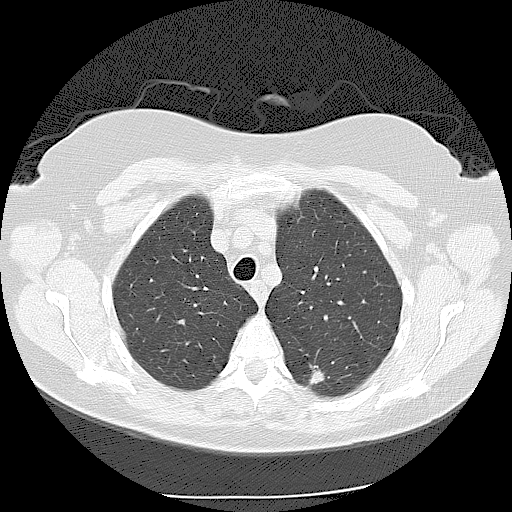
Low-dose screening chest CT, one axial slice; slice 89 of 116 in the series (ordered by position); 120 kVp; lung window (W 1500 / L -600 HU); 2.5 mm slice thickness; 512 × 512 image matrix, field of view 360 × 360 mm.
Outlined on this slice (outlined manually by an expert reader):
- lesion 1 (tumor, lower lobe of left lung): bounding box <309,364,330,386> (left, top, right, bottom; pixels)